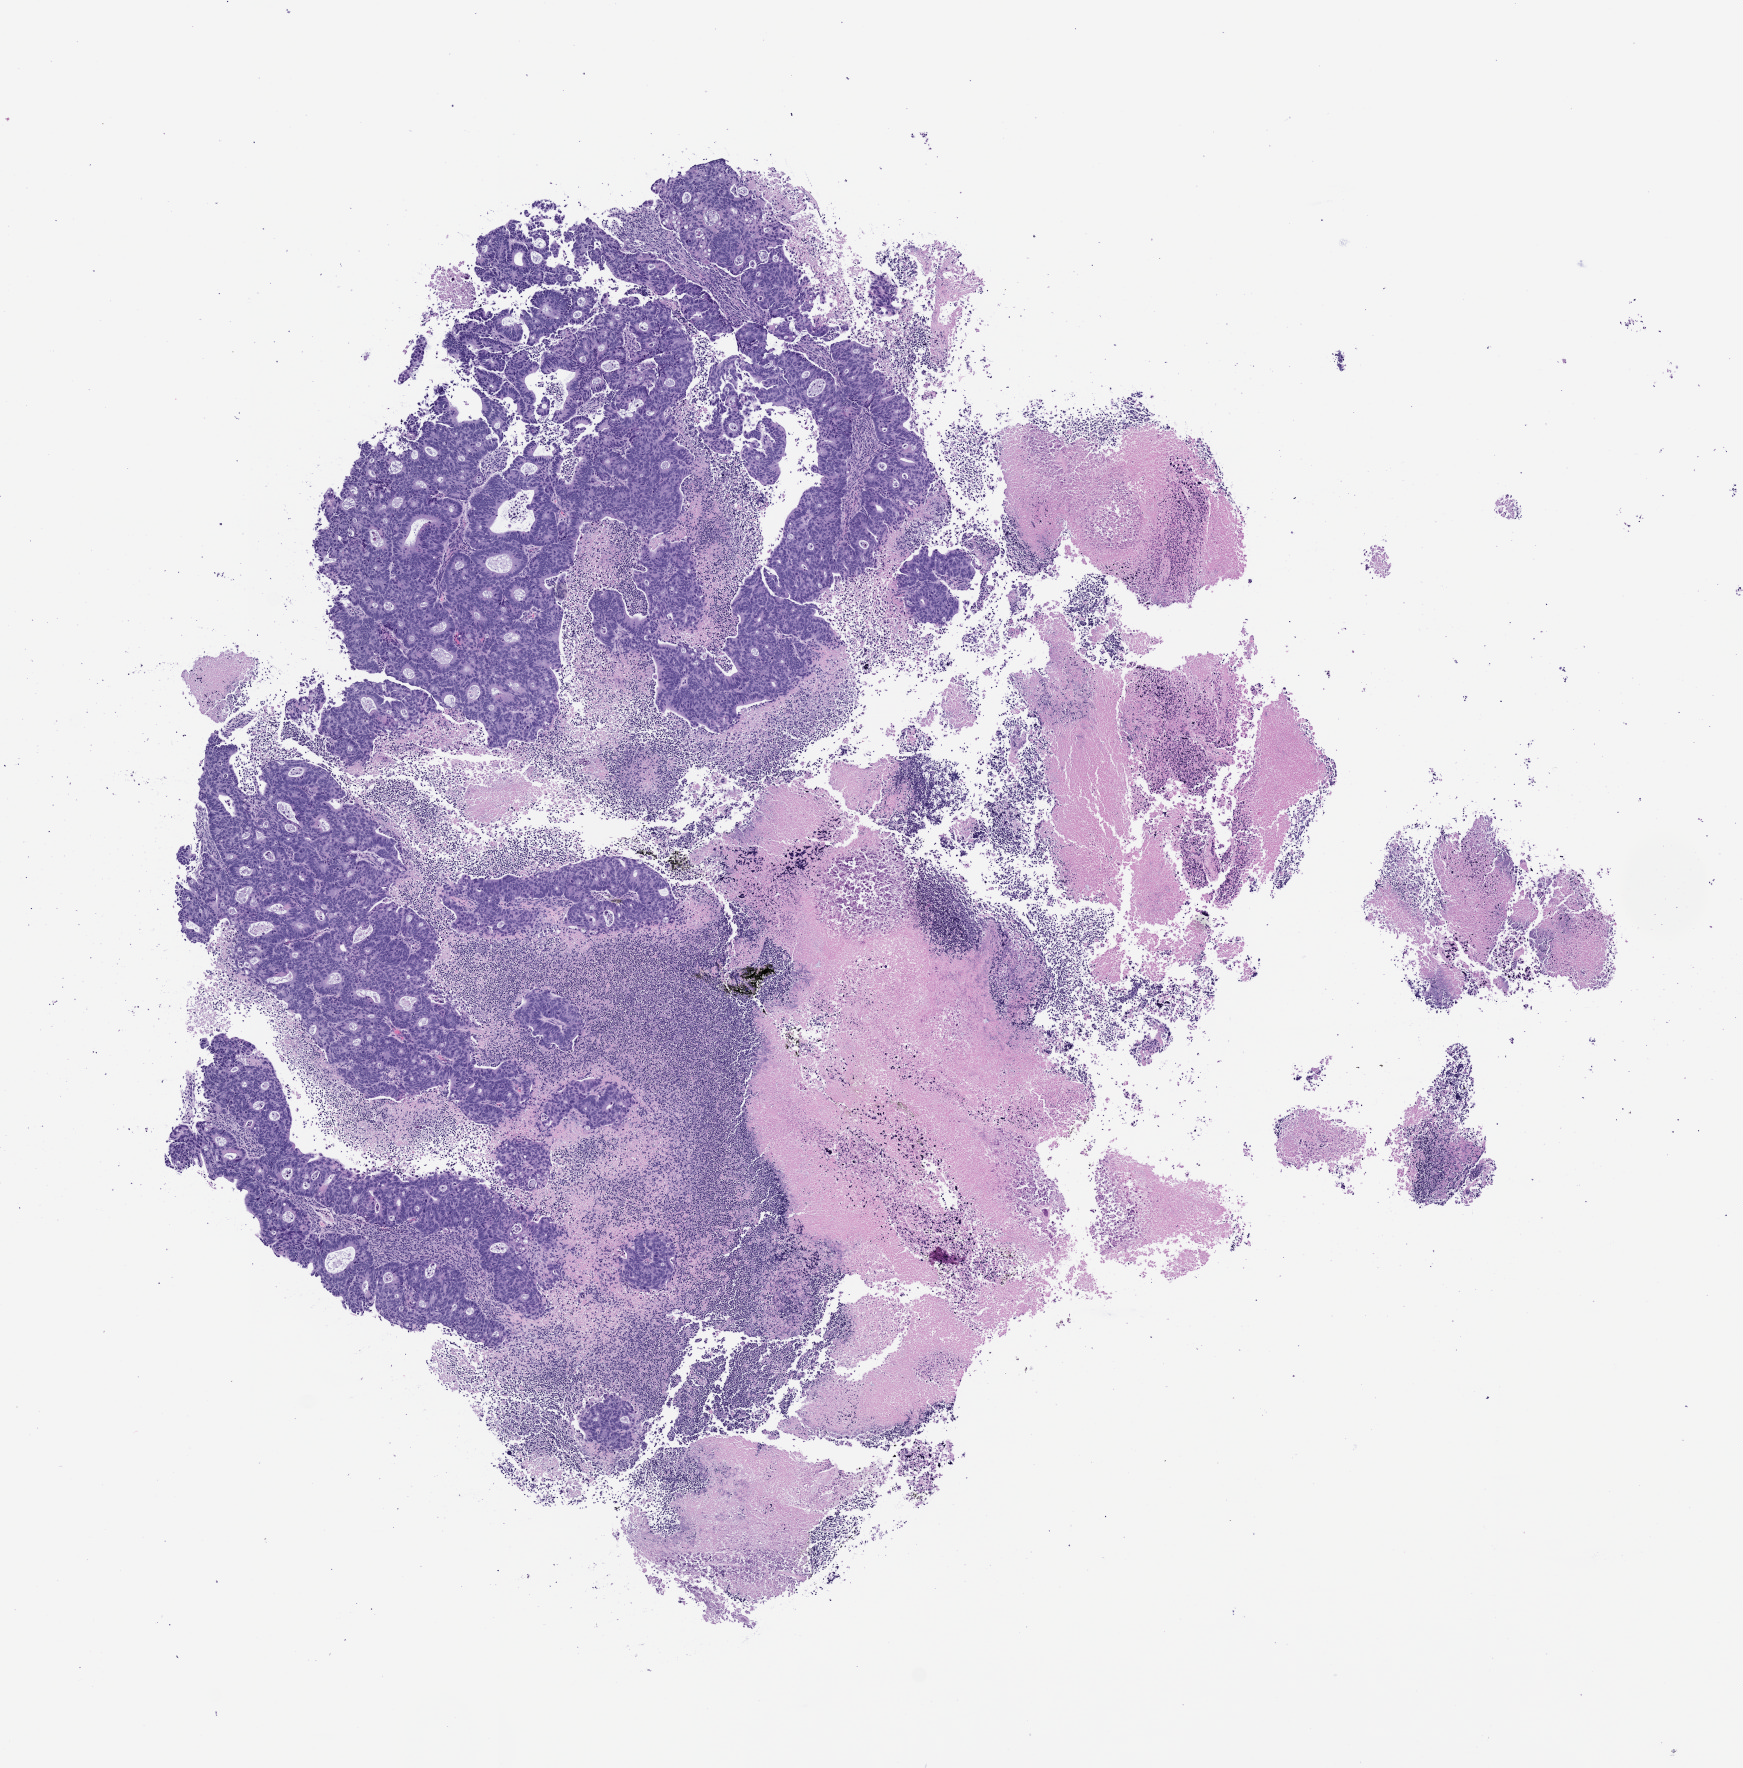
Whole-slide image, H&E: patient-derived xenograft (human tumor grown in a mouse), passage 0 — low-resolution overview of the scanned area, about 7.0 x 7.1 mm, formalin-fixed paraffin-embedded section, tumor site category: colon.
Originating patient diagnosis: Colon Adenocarcinoma.